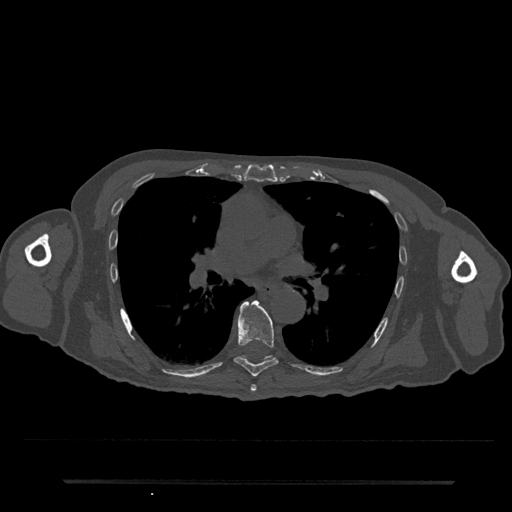
CT including the spine, one axial slice. Position 474 of 797 along the scan axis. Reconstruction kernel Br40s/3. 120 kVp. Bone window (W 1800 / L 400 HU). 512 × 512 image matrix, field of view 427 × 427 mm. Patient: male, 74 years. From the clinical record (not read from this slice): primary cancer: prostate.
Annotated regions visible in this slice (semi-automatic segmentation, software-assisted and operator-edited):
- T6 vertebra: bounding box (x1, y1, x2, y2) in pixels: (250, 385, 257, 392)
- T7 vertebra: (234, 300, 279, 377)
- T8 vertebra: (242, 356, 274, 361)